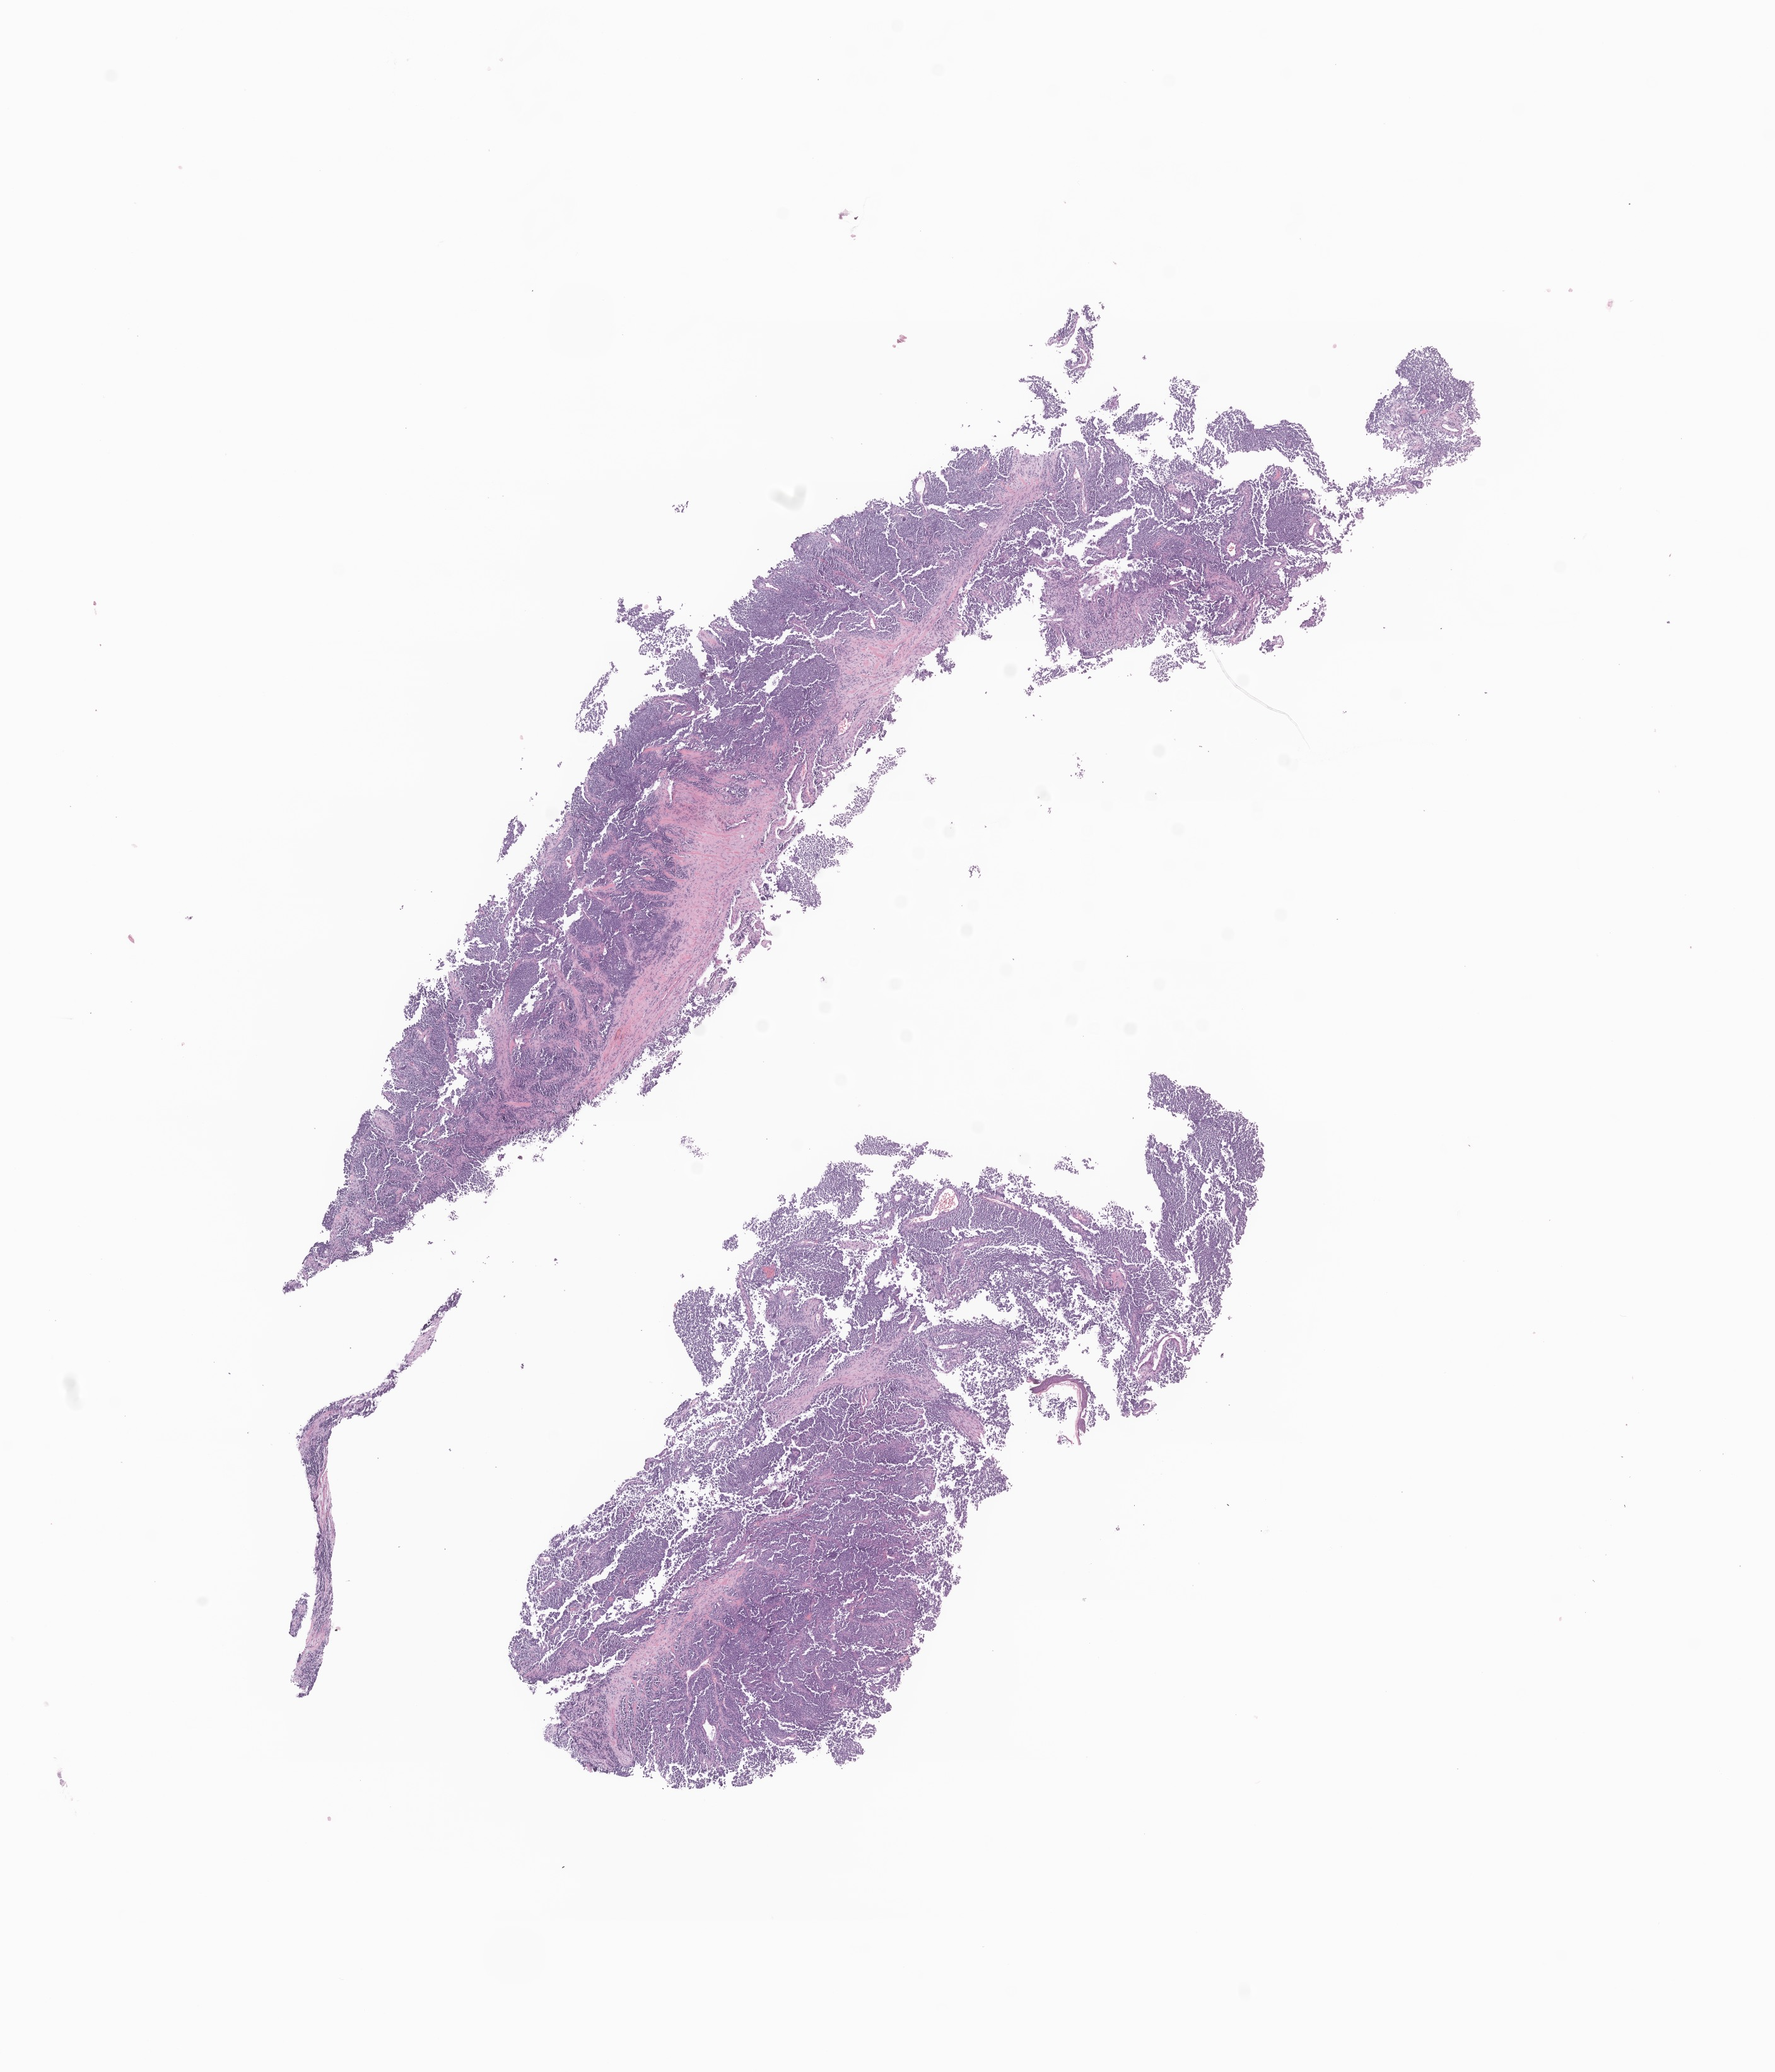
Haematoxylin and eosin whole-slide image of tumor tissue from the head and neck — shown as a low-resolution overview of the whole scanned area (about 11.9 x 13.8 mm). FFPE section. Patient: male, age 116 months (9 years 8 months).
- recorded diagnosis: Rhabdomyosarcoma, NOS